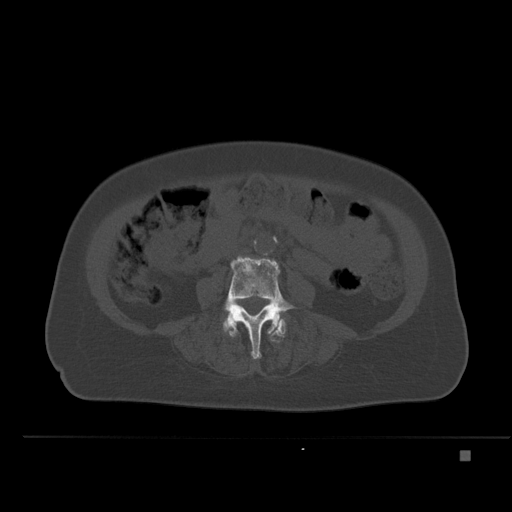
CT including the spine, one axial slice. Slice 178 of 477 in the series (ordered by position). Bone window (W 1800 / L 400 HU). 512 × 512 image matrix, field of view 422 × 422 mm. Female patient, age 74 years. From the clinical record (not read from this slice): primary cancer: colon.
Structures marked on this image (semi-automatic segmentation, software-assisted and operator-edited):
- L4 vertebra: bounding box (x1, y1, x2, y2) in pixels: (223, 257, 297, 359)
- L5 vertebra: (223, 319, 286, 342)